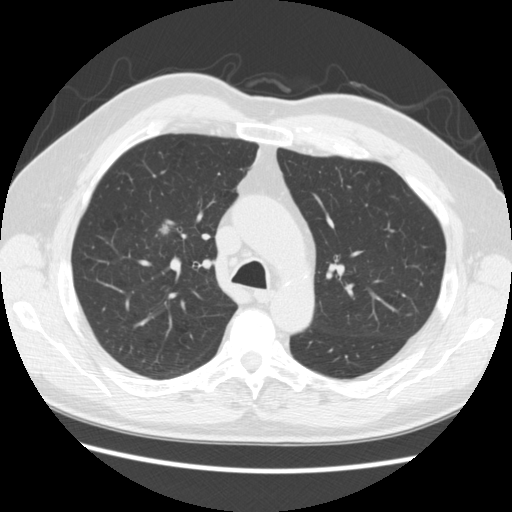
Low-dose screening chest CT, axial slice. Baseline screening round. Lung window (W 1500 / L -600 HU). 120 kVp. Slice 81 of 259 in the series. 512 × 512 image matrix, field of view 360 × 360 mm. Male, age 69 years at enrolment.
• Expert reader's lesion annotation, bounding box <151,214,190,245> (left, top, right, bottom; pixels).
• The exam's reader record, not a measurement of the box and not confirmed to be the same lesion: non-calcified nodule or mass ≥4 mm, right upper lobe, 9 × 7 mm, poorly defined margins, soft tissue attenuation.
• Official screen result: positive, change unspecified: nodule(s) >= 4 mm or enlarging nodule(s), mass(es), or other non-specific abnormalities suspicious for lung cancer.
• Later outcome: lung cancer diagnosed 50 days after this screen — adenocarcinoma, NOS, right upper lobe, moderately differentiated (G2), stage IA (AJCC 6th edition), 9 mm at pathology.